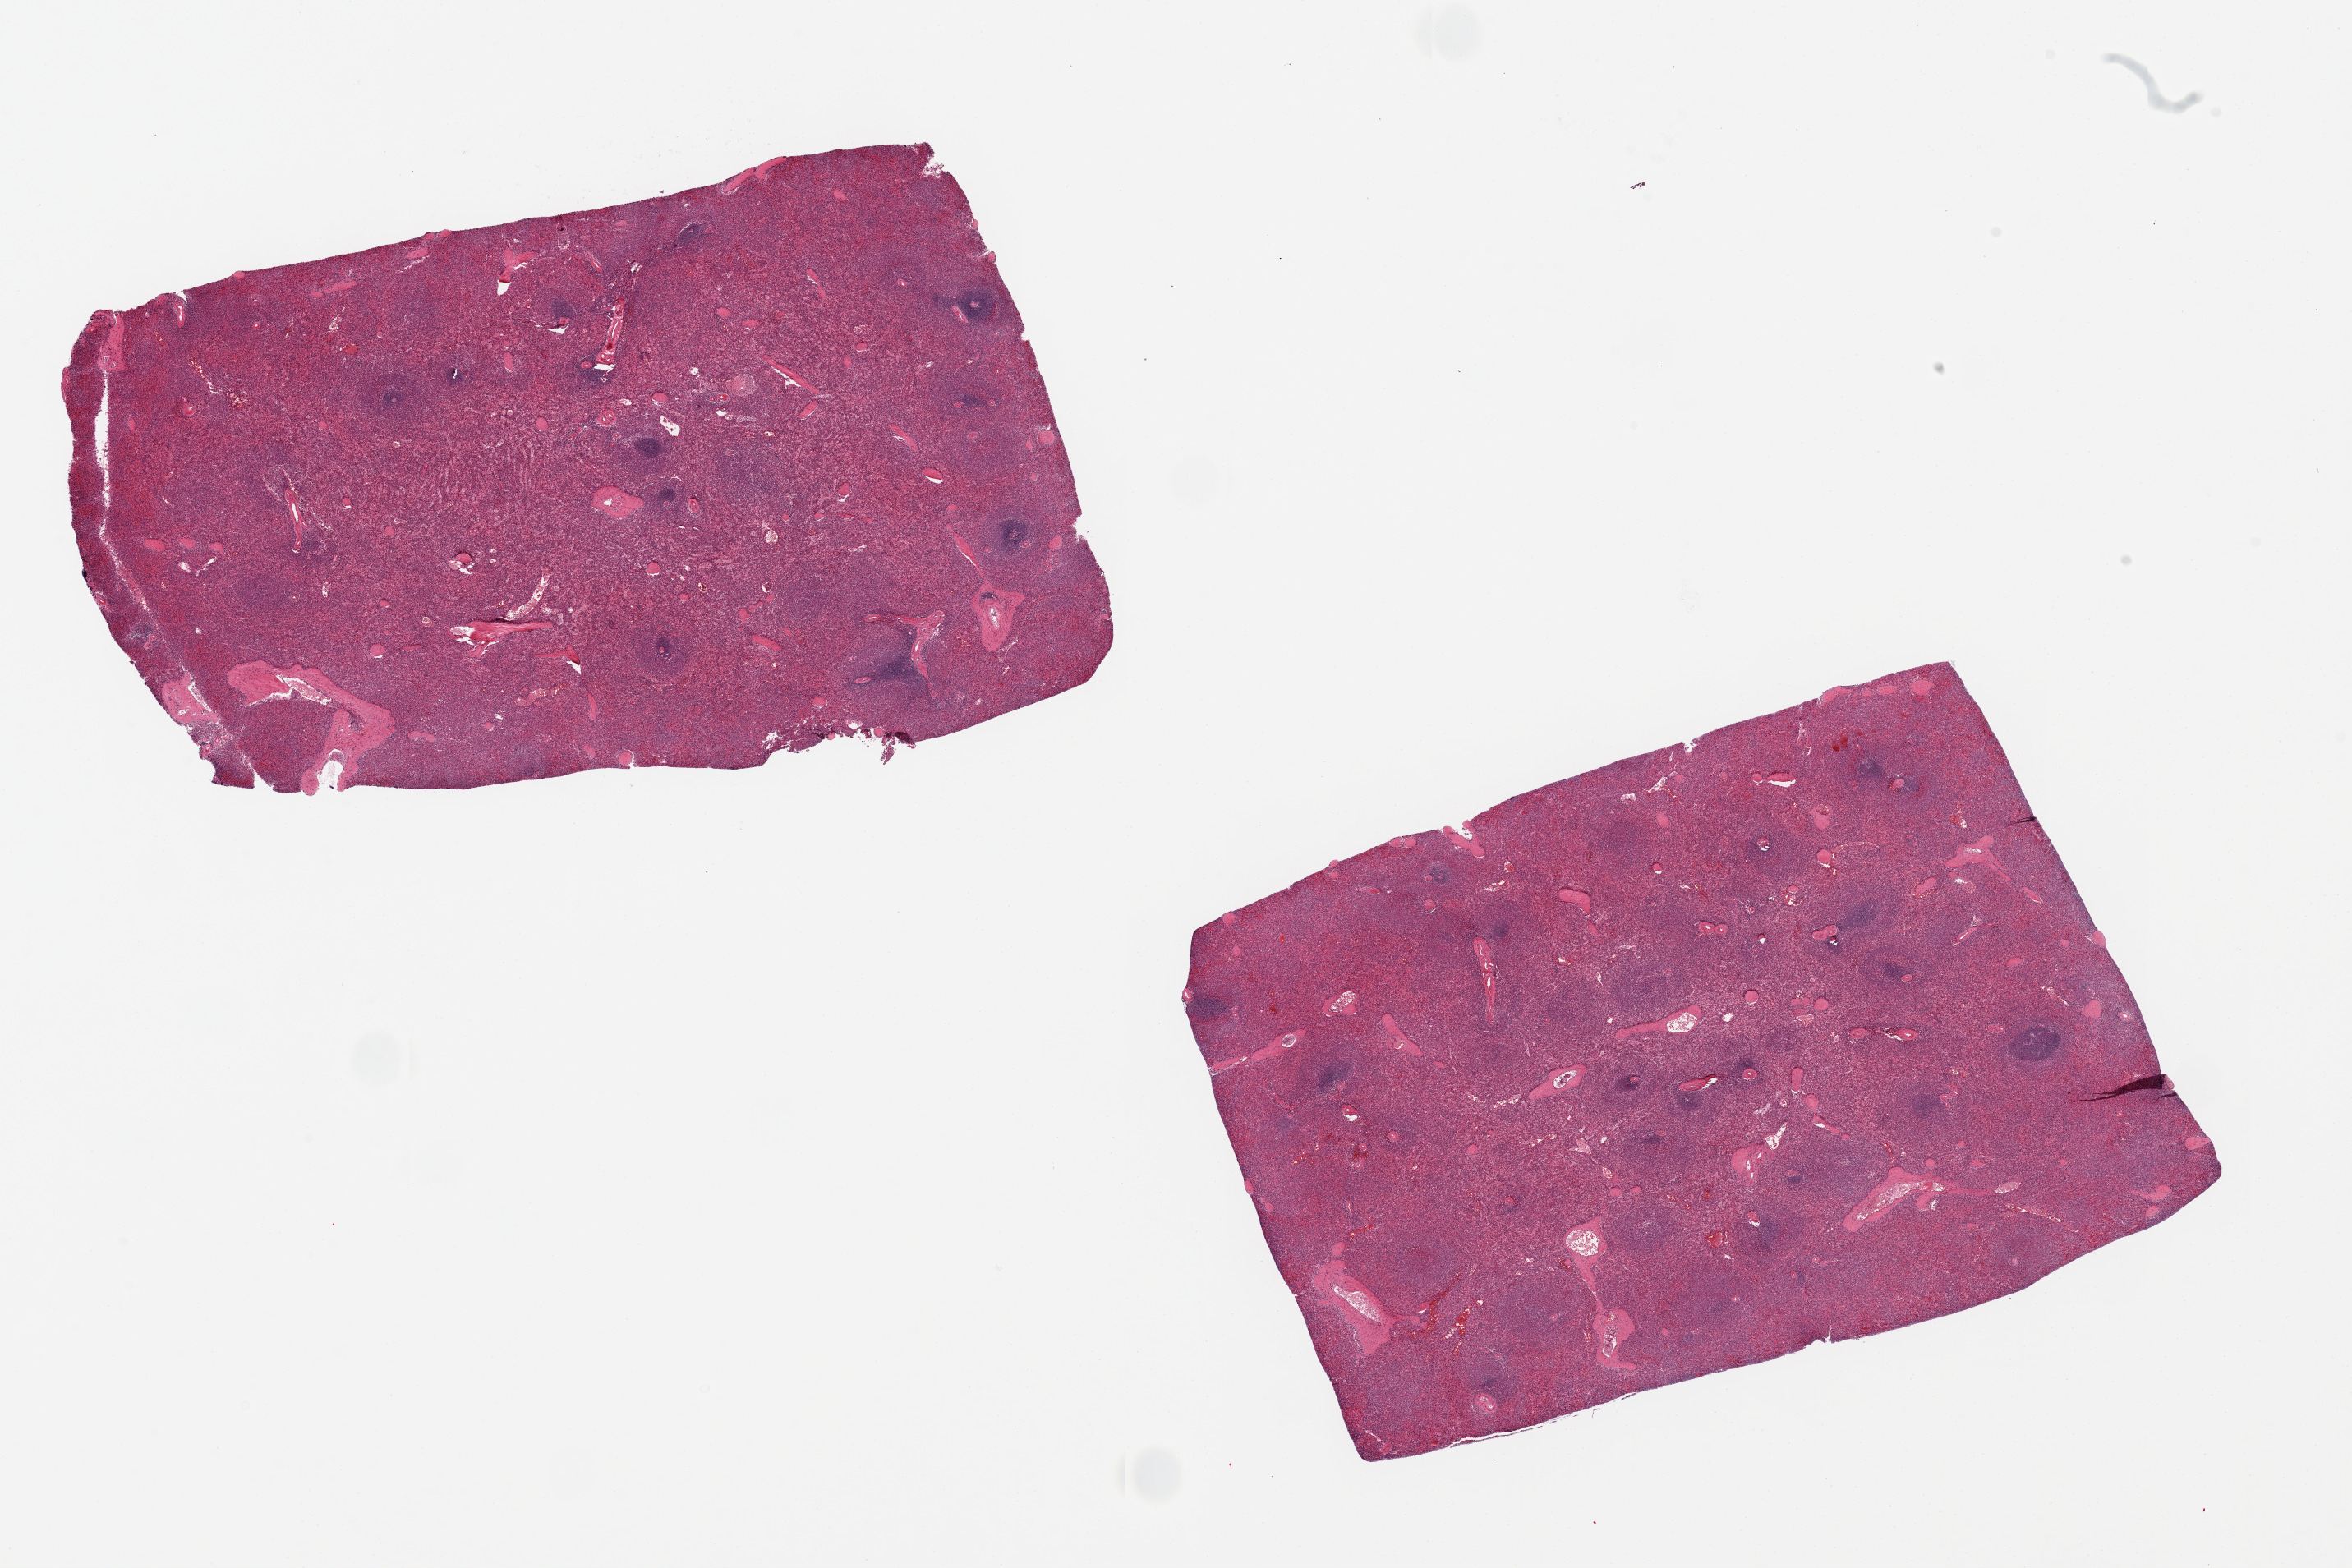
Haematoxylin and eosin whole-slide image, brightfield — shown as a low-resolution overview of the whole scanned area (about 22.6 x 15.1 mm). PAXgene-fixed paraffin-embedded (PFPE) section. Target tissue: spleen. Tissue donor sample. Donor: female.
Review note (as recorded): 2 pieces, 9x5 & 8x6 mm; not overly congested.